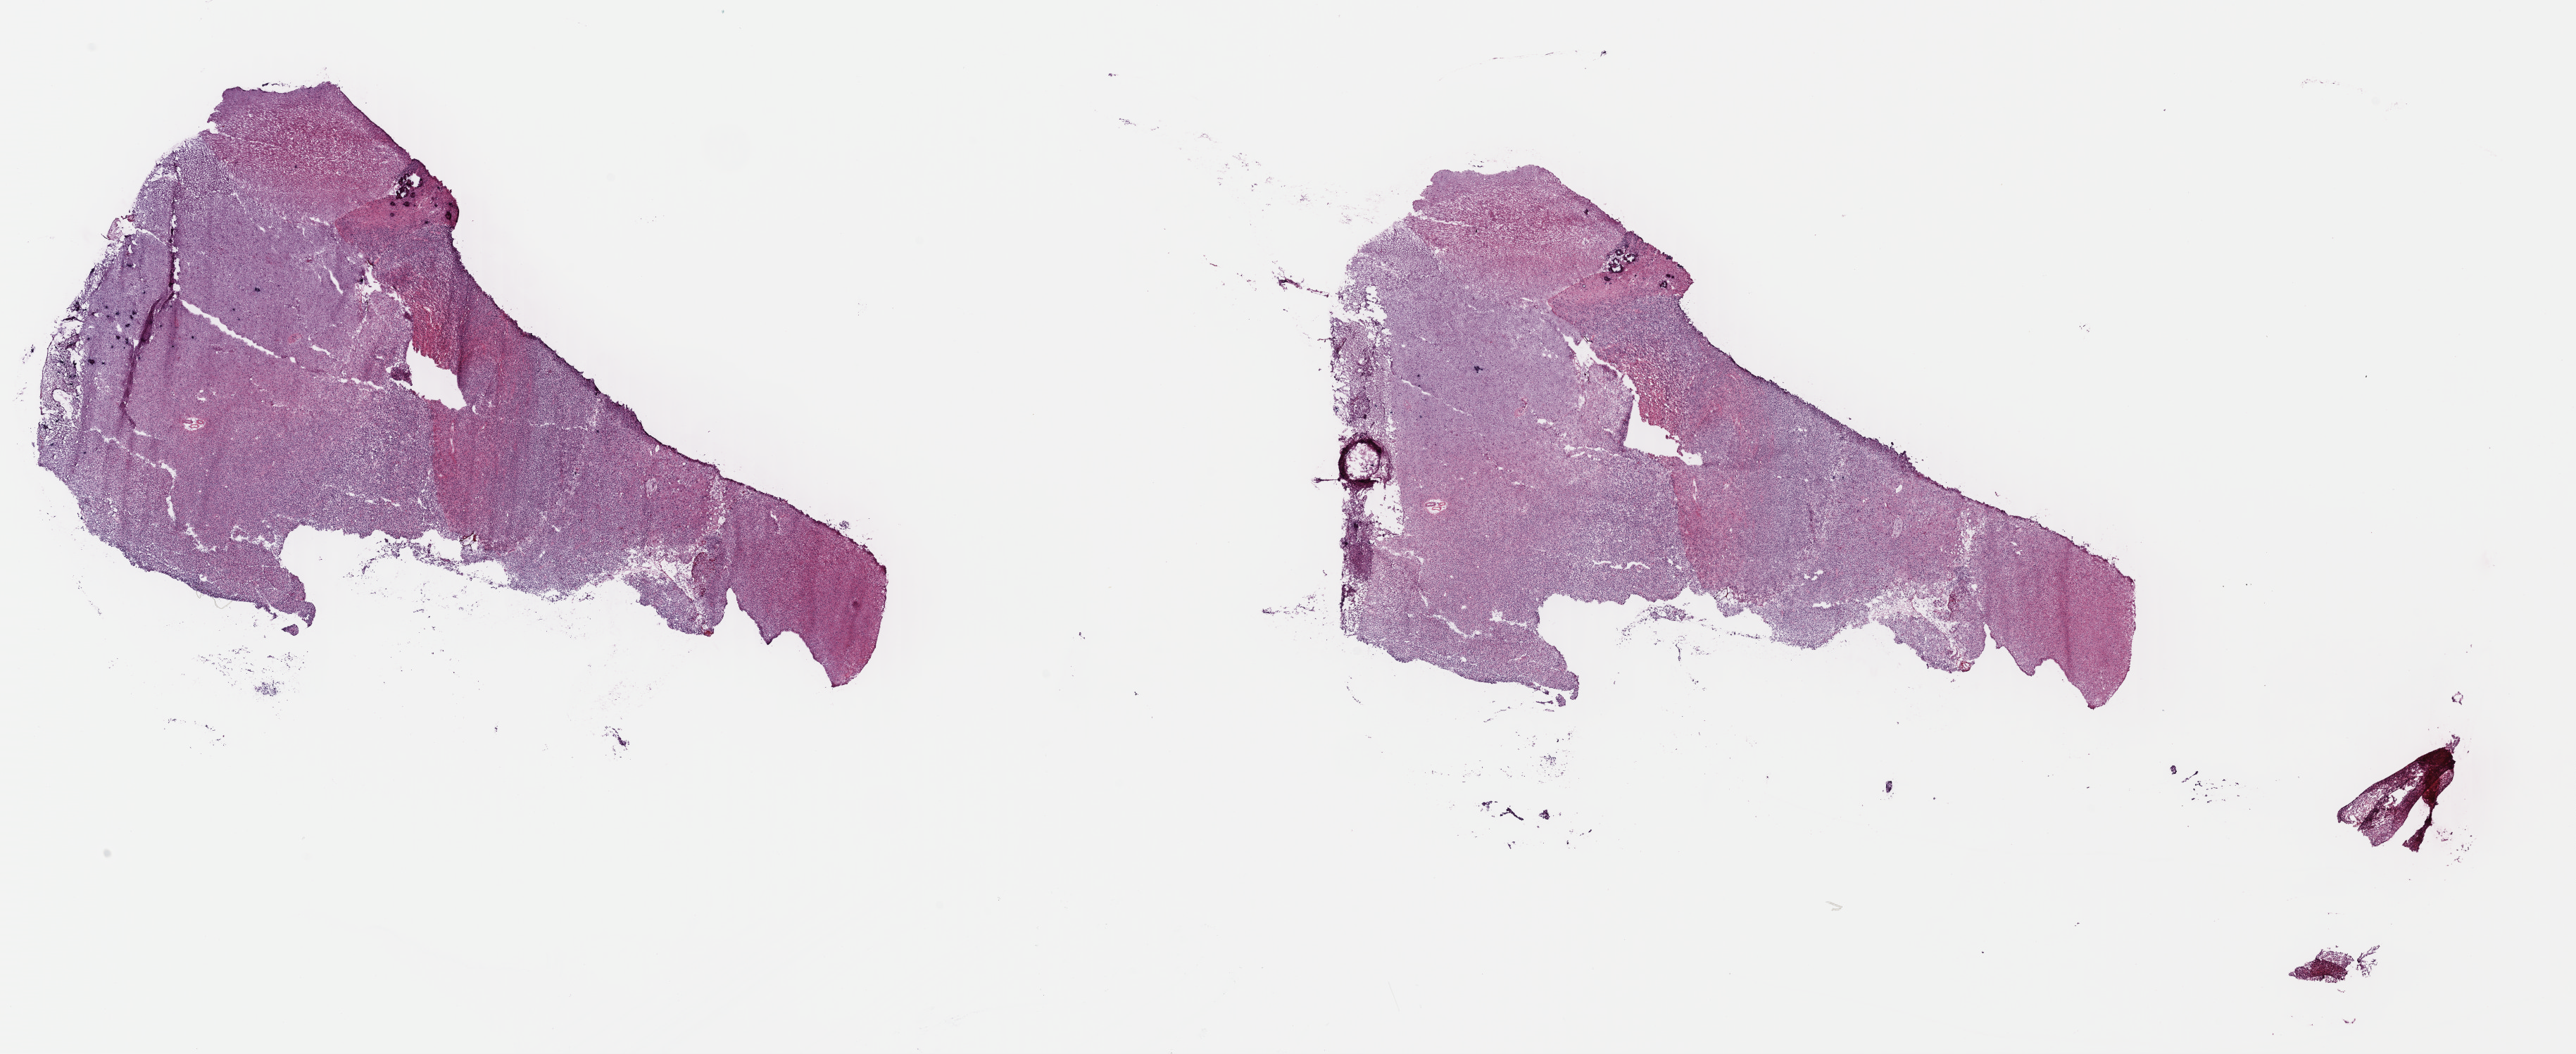
Digitized H&E tissue section (whole slide), whole scanned area (about 28.8 x 11.8 mm) shown as a low-resolution overview. Frozen section. Primary tumour sample from the brain. Female, age 74 years at initial diagnosis. Histologic grade: G3 (poorly differentiated). Pathologist review of this section (percent, as recorded): tumour cells 60%, tumour nuclei 90%, normal cells 10%, stromal cells 30%, necrosis 0%. Inflammatory infiltration, as recorded: lymphocyte infiltration 0%, monocyte infiltration 0%, neutrophil infiltration 0%.
Histologic diagnosis: Oligodendroglioma, anaplastic (cerebrum).